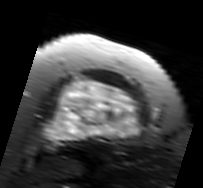
MRI of an extremity soft-tissue mass, one axial slice. Position 58 of 91 along the scan axis. T2-weighted fat-saturated. MR volume resampled by the dataset authors to the PET/CT grid (not the native acquisition matrix). 203 × 188 image matrix. Female patient. From the clinical record (not read from this slice): histological type: malignant solitary fibrous tumor; grade: intermediate; site of the primary tumour: right thigh.
Outlined on this slice (expert contour drawn on MRI and transferred to this co-registered scan by the dataset authors):
- gross tumour volume including surrounding oedema: bounding box (x1, y1, x2, y2) in pixels: (44, 76, 144, 146)
- gross tumour volume (mass): (44, 79, 141, 146)